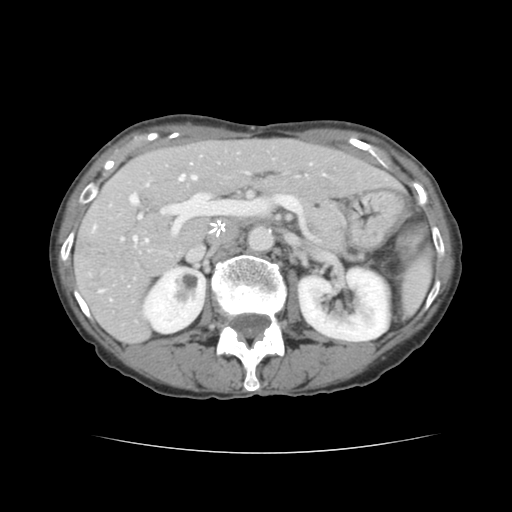
Contrast-enhanced abdominal CT, one axial slice; slice 76 of 136 in the series (ordered by position); 120 kVp; intravenous contrast given; soft-tissue window (W 400 / L 40 HU); 2.5 mm slice thickness; 512 × 512 image matrix, field of view 319 × 319 mm. Female patient, age 77 years. Case-level facts recorded for this patient, not image findings: diagnosis: colorectal cancer liver metastases, imaged before liver resection; multiple liver metastases: yes; largest metastasis: 3 cm; chemotherapy before resection: yes.
Structures marked on this image (outlined manually by an expert reader):
- hepatic veins: bounding box <134,175,196,239> (left, top, right, bottom; pixels)
- liver: <75,140,396,341>
- planned liver remnant (the part of the liver to remain after resection): <155,140,394,199>
- portal vein (with intrahepatic branches): <94,184,238,292>